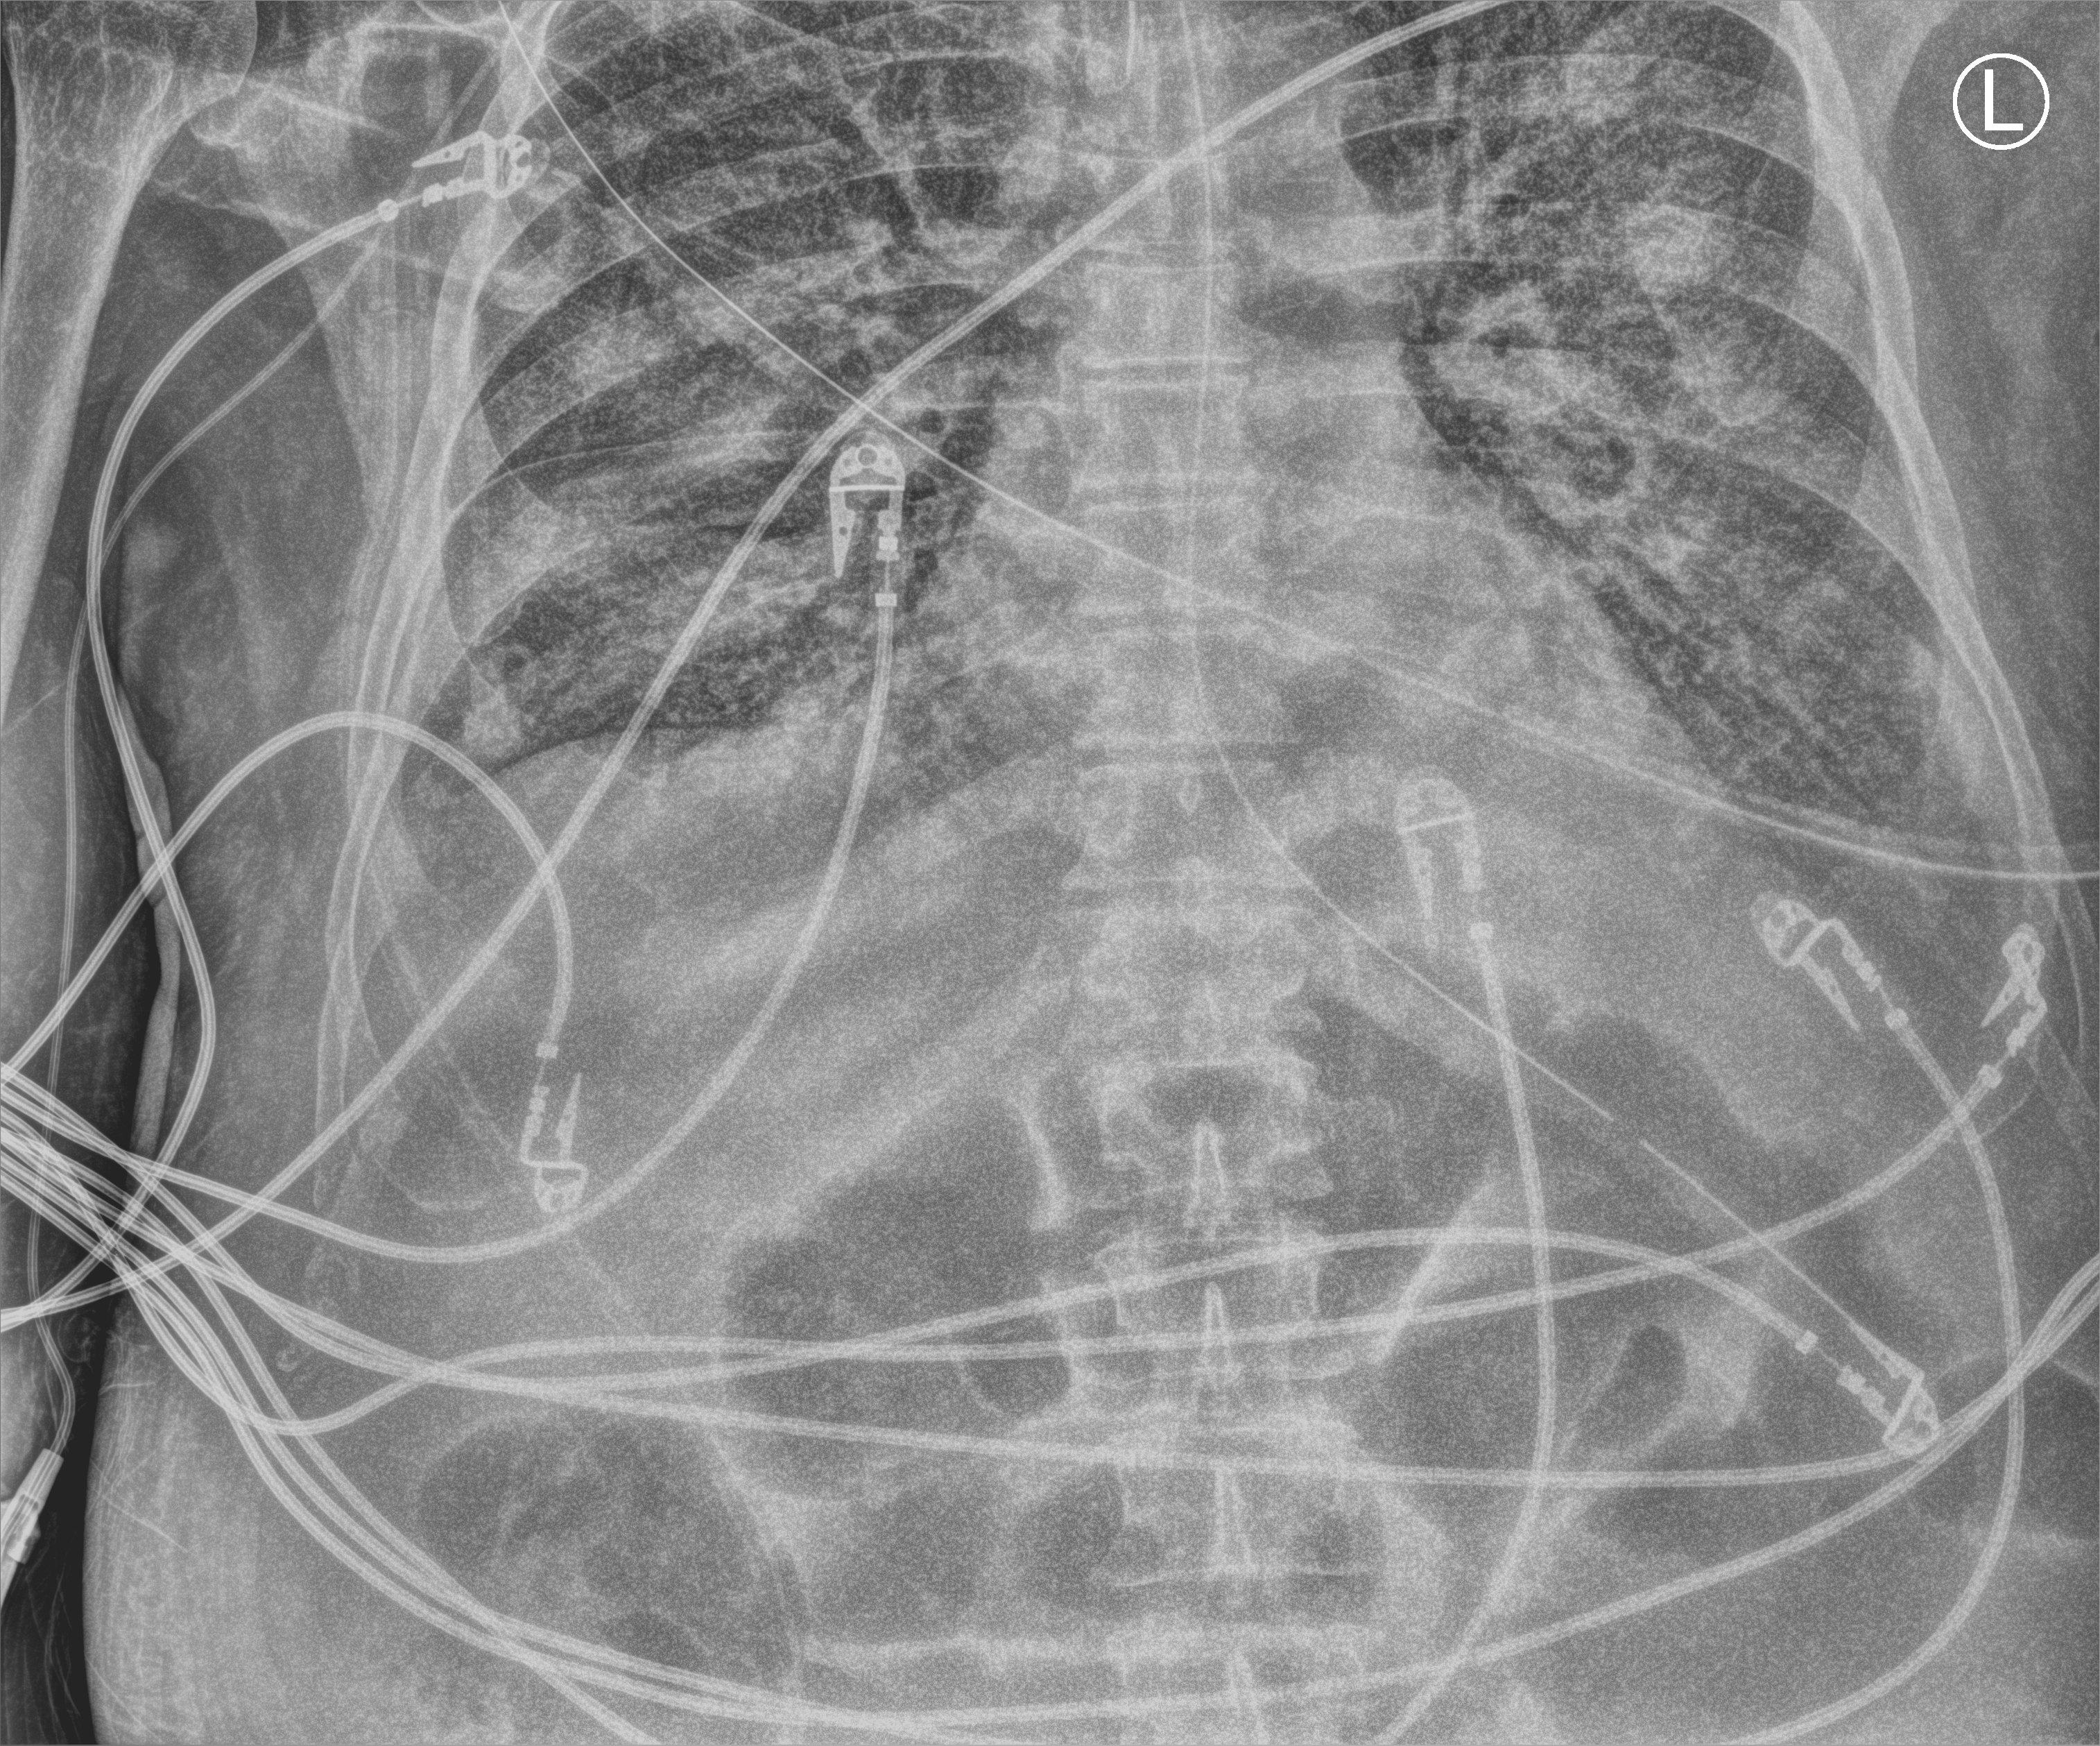
Bedside chest radiograph (computed radiography), anteroposterior (AP) projection. Patient hospitalised with COVID-19; male, aged 60–74 years.
Admission-level facts for this patient (not findings on this image; timing relative to this image not recorded):
- length of hospital stay: 24 days
- admitted to intensive care during this hospital stay: yes
- mechanically ventilated during this hospital stay: yes